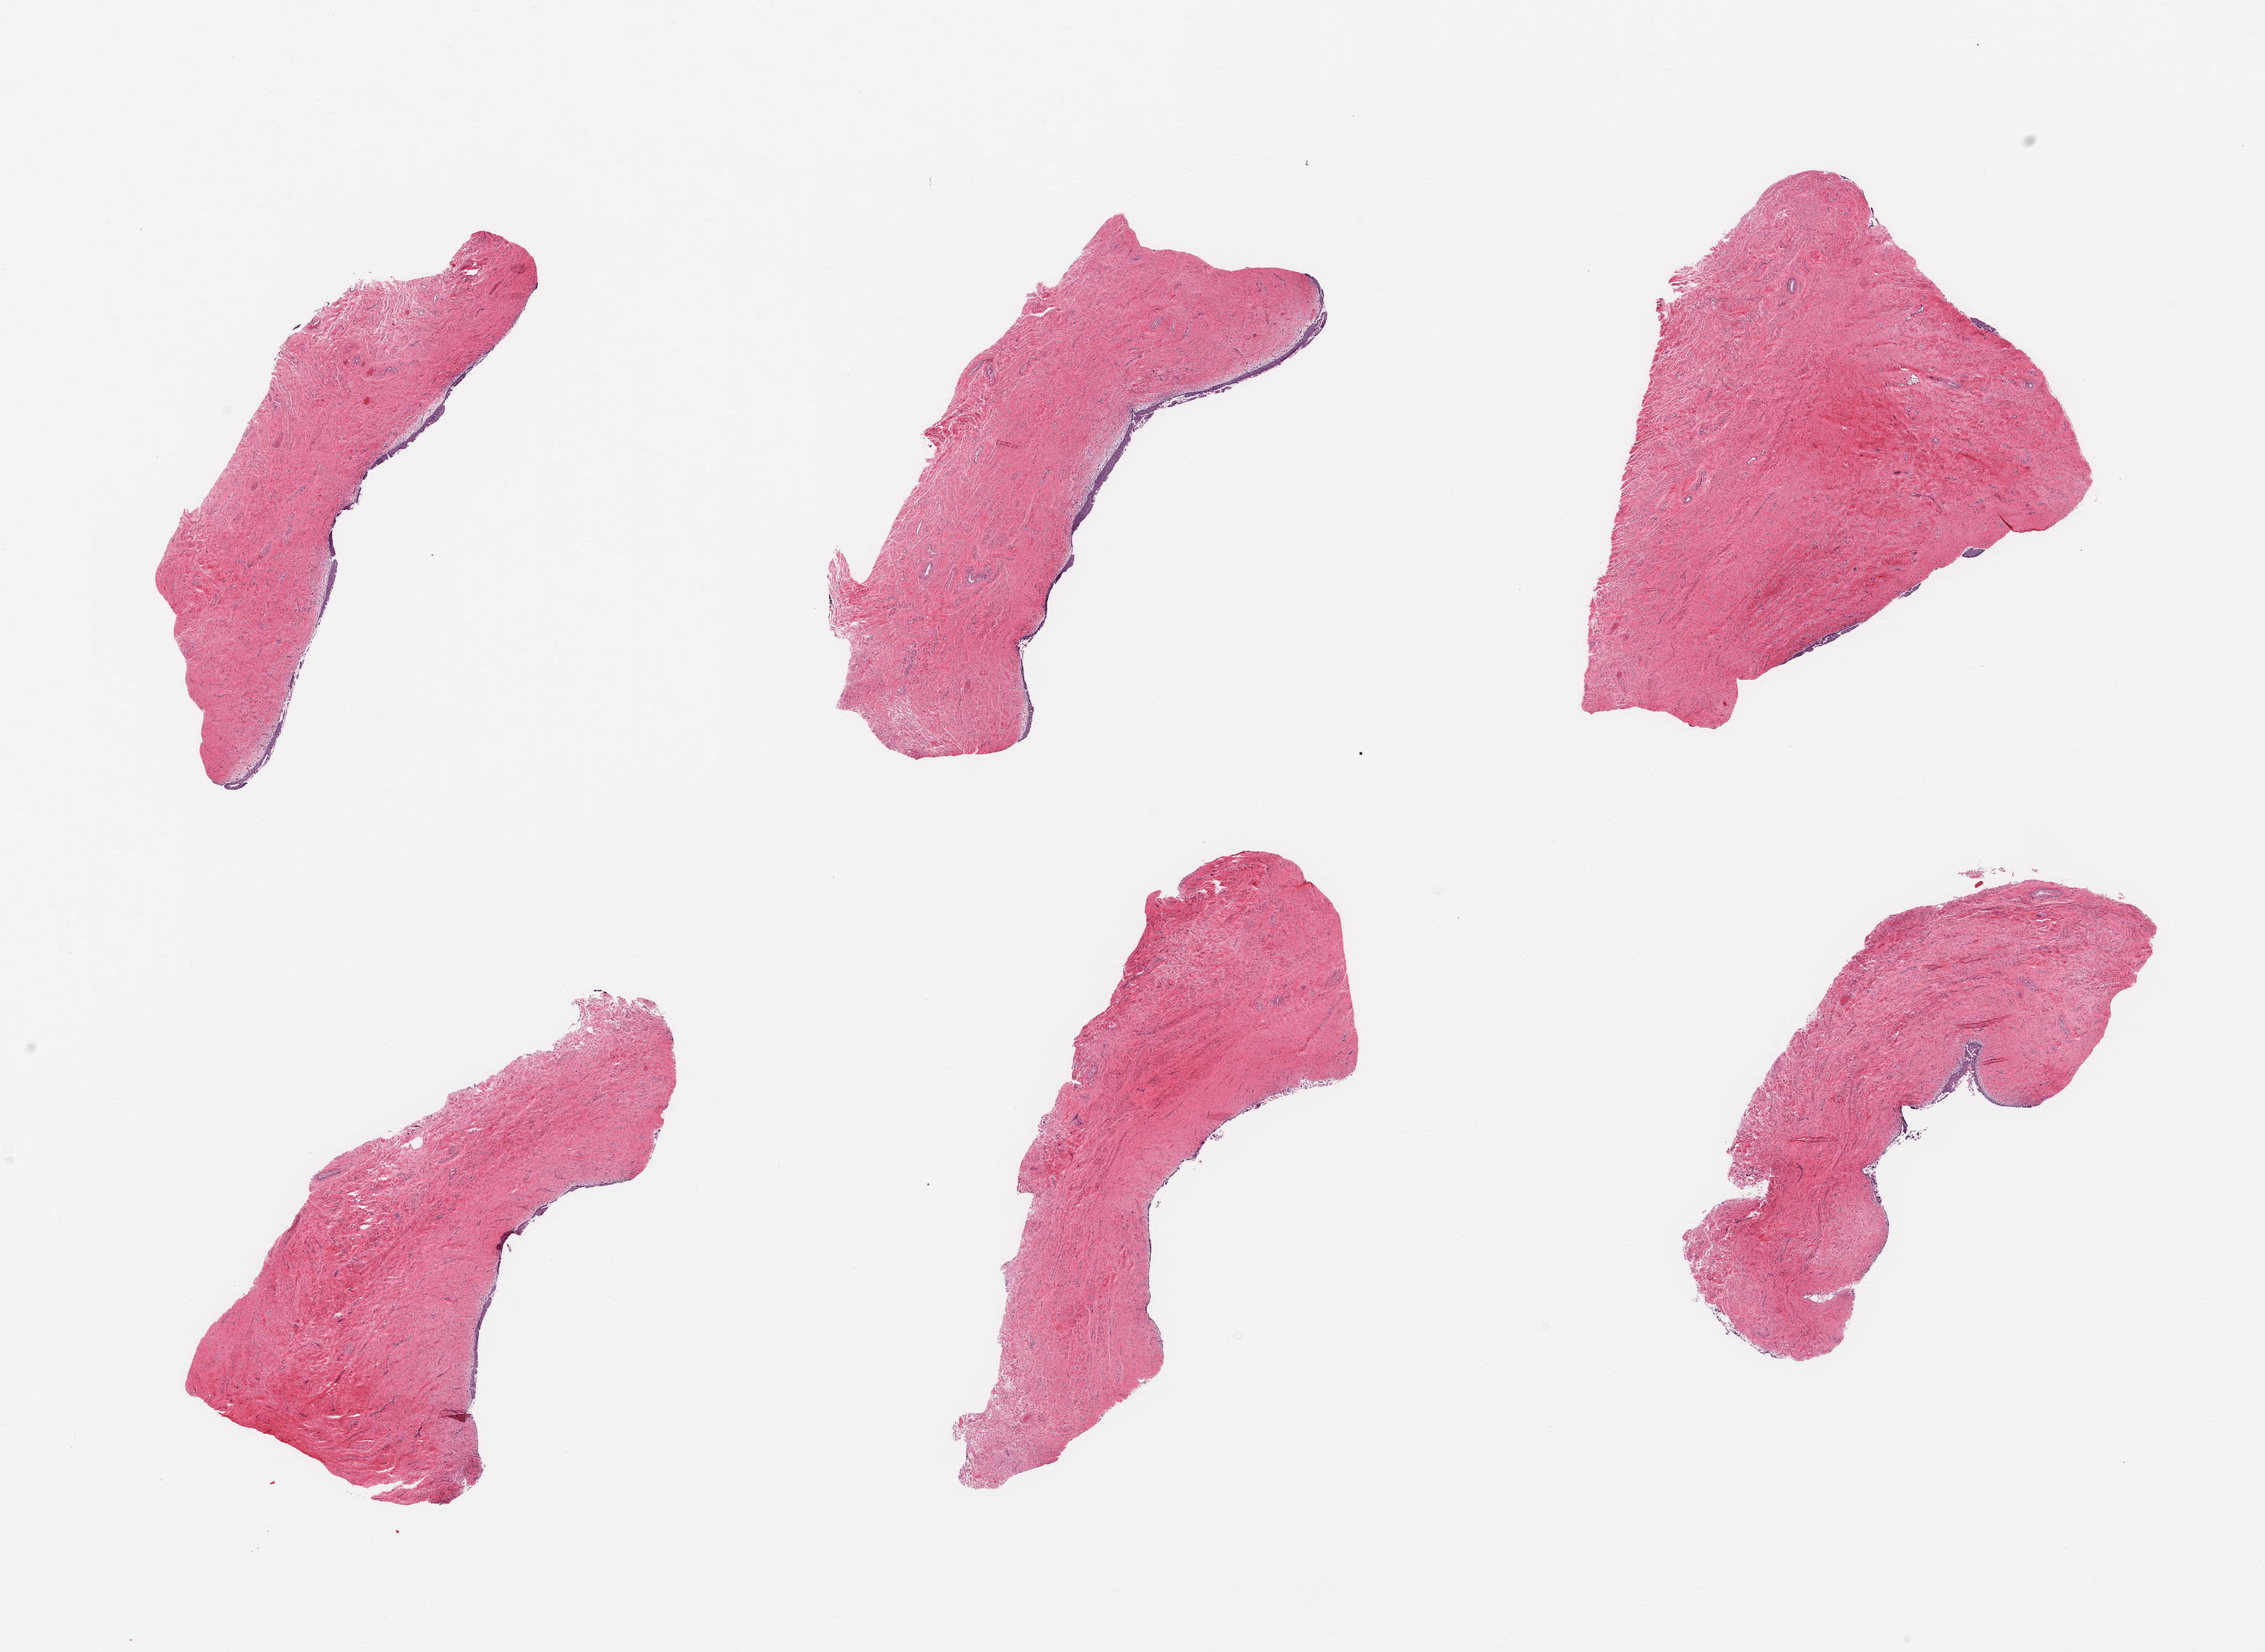
Whole-slide image, H&E stain, whole scanned area (about 24.6 x 18.0 mm, acquisition: 20x scan) shown as a low-resolution overview. PAXgene-fixed, paraffin-embedded tissue. Target tissue: vagina. Tissue donor sample. Female donor.
Review note (as recorded): 6 pieces; epithelium largely sloughed.